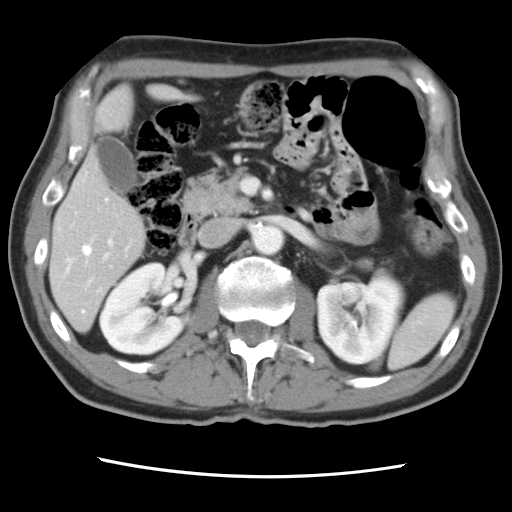
Contrast-enhanced abdominal CT, one axial slice. Slice 38 of 83 in the series (ordered by position). Intravenous contrast given. Soft-tissue window (W 400 / L 40 HU). 512 × 512 image matrix, field of view 321 × 321 mm. Male patient, age 69 years. From the clinical record (not read from this slice): diagnosis: colorectal cancer liver metastases, imaged before liver resection; multiple liver metastases: yes.
Annotated regions visible in this slice (outlined manually by an expert reader):
- hepatic veins: bounding box <82,199,108,312> (left, top, right, bottom; pixels)
- liver: <52,90,147,329>
- planned liver remnant (the part of the liver to remain after resection): <52,156,147,329>
- portal vein (with intrahepatic branches): <82,175,114,288>